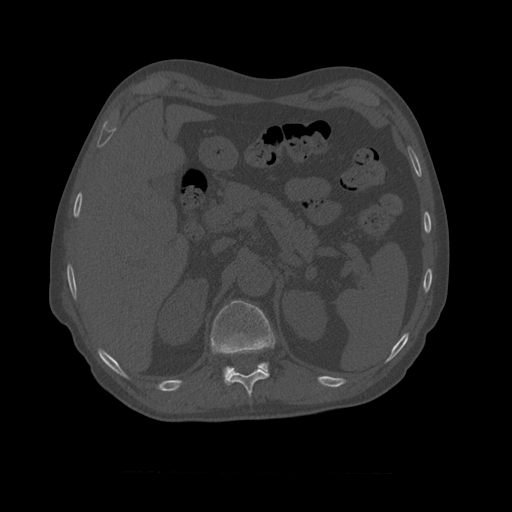
CT including the spine, one axial slice. Slice 392 of 450 in the series (ordered by position). Reconstruction kernel STANDARD. Bone window (W 1800 / L 400 HU). 1.25 mm slice thickness. 512 × 512 image matrix. Patient age 75 years. Case-level facts recorded for this patient, not image findings: primary cancer: prostate.
Outlined on this slice (semi-automatic segmentation, software-assisted and operator-edited):
- T10 vertebra: box from (x=225, y=349) to (x=270, y=398) px
- T11 vertebra: (x=211, y=300)–(x=276, y=382)